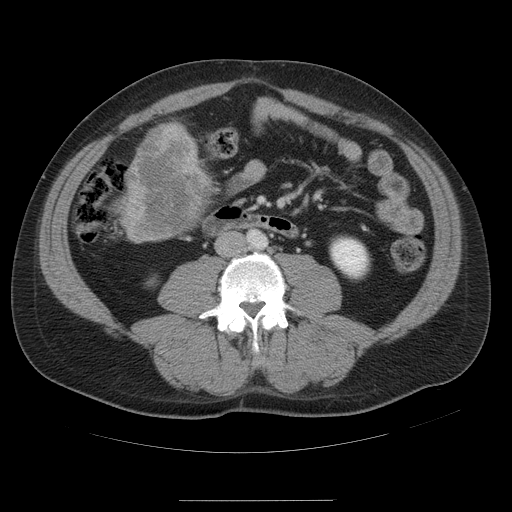
Contrast-enhanced abdominal CT, one axial slice. Position 8 of 54 along the scan axis. 120 kVp. Intravenous contrast given. Soft-tissue window (W 400 / L 40 HU). 512 × 512 image matrix, field of view 436 × 436 mm. Male patient, age 40 years. From the clinical record (not read from this slice): diagnosis: colorectal cancer liver metastases, imaged before liver resection.
Annotated regions visible in this slice (outlined manually by an expert reader):
- liver: box from (x=123, y=124) to (x=212, y=243) px
- liver metastasis: (x=127, y=130)–(x=206, y=241)